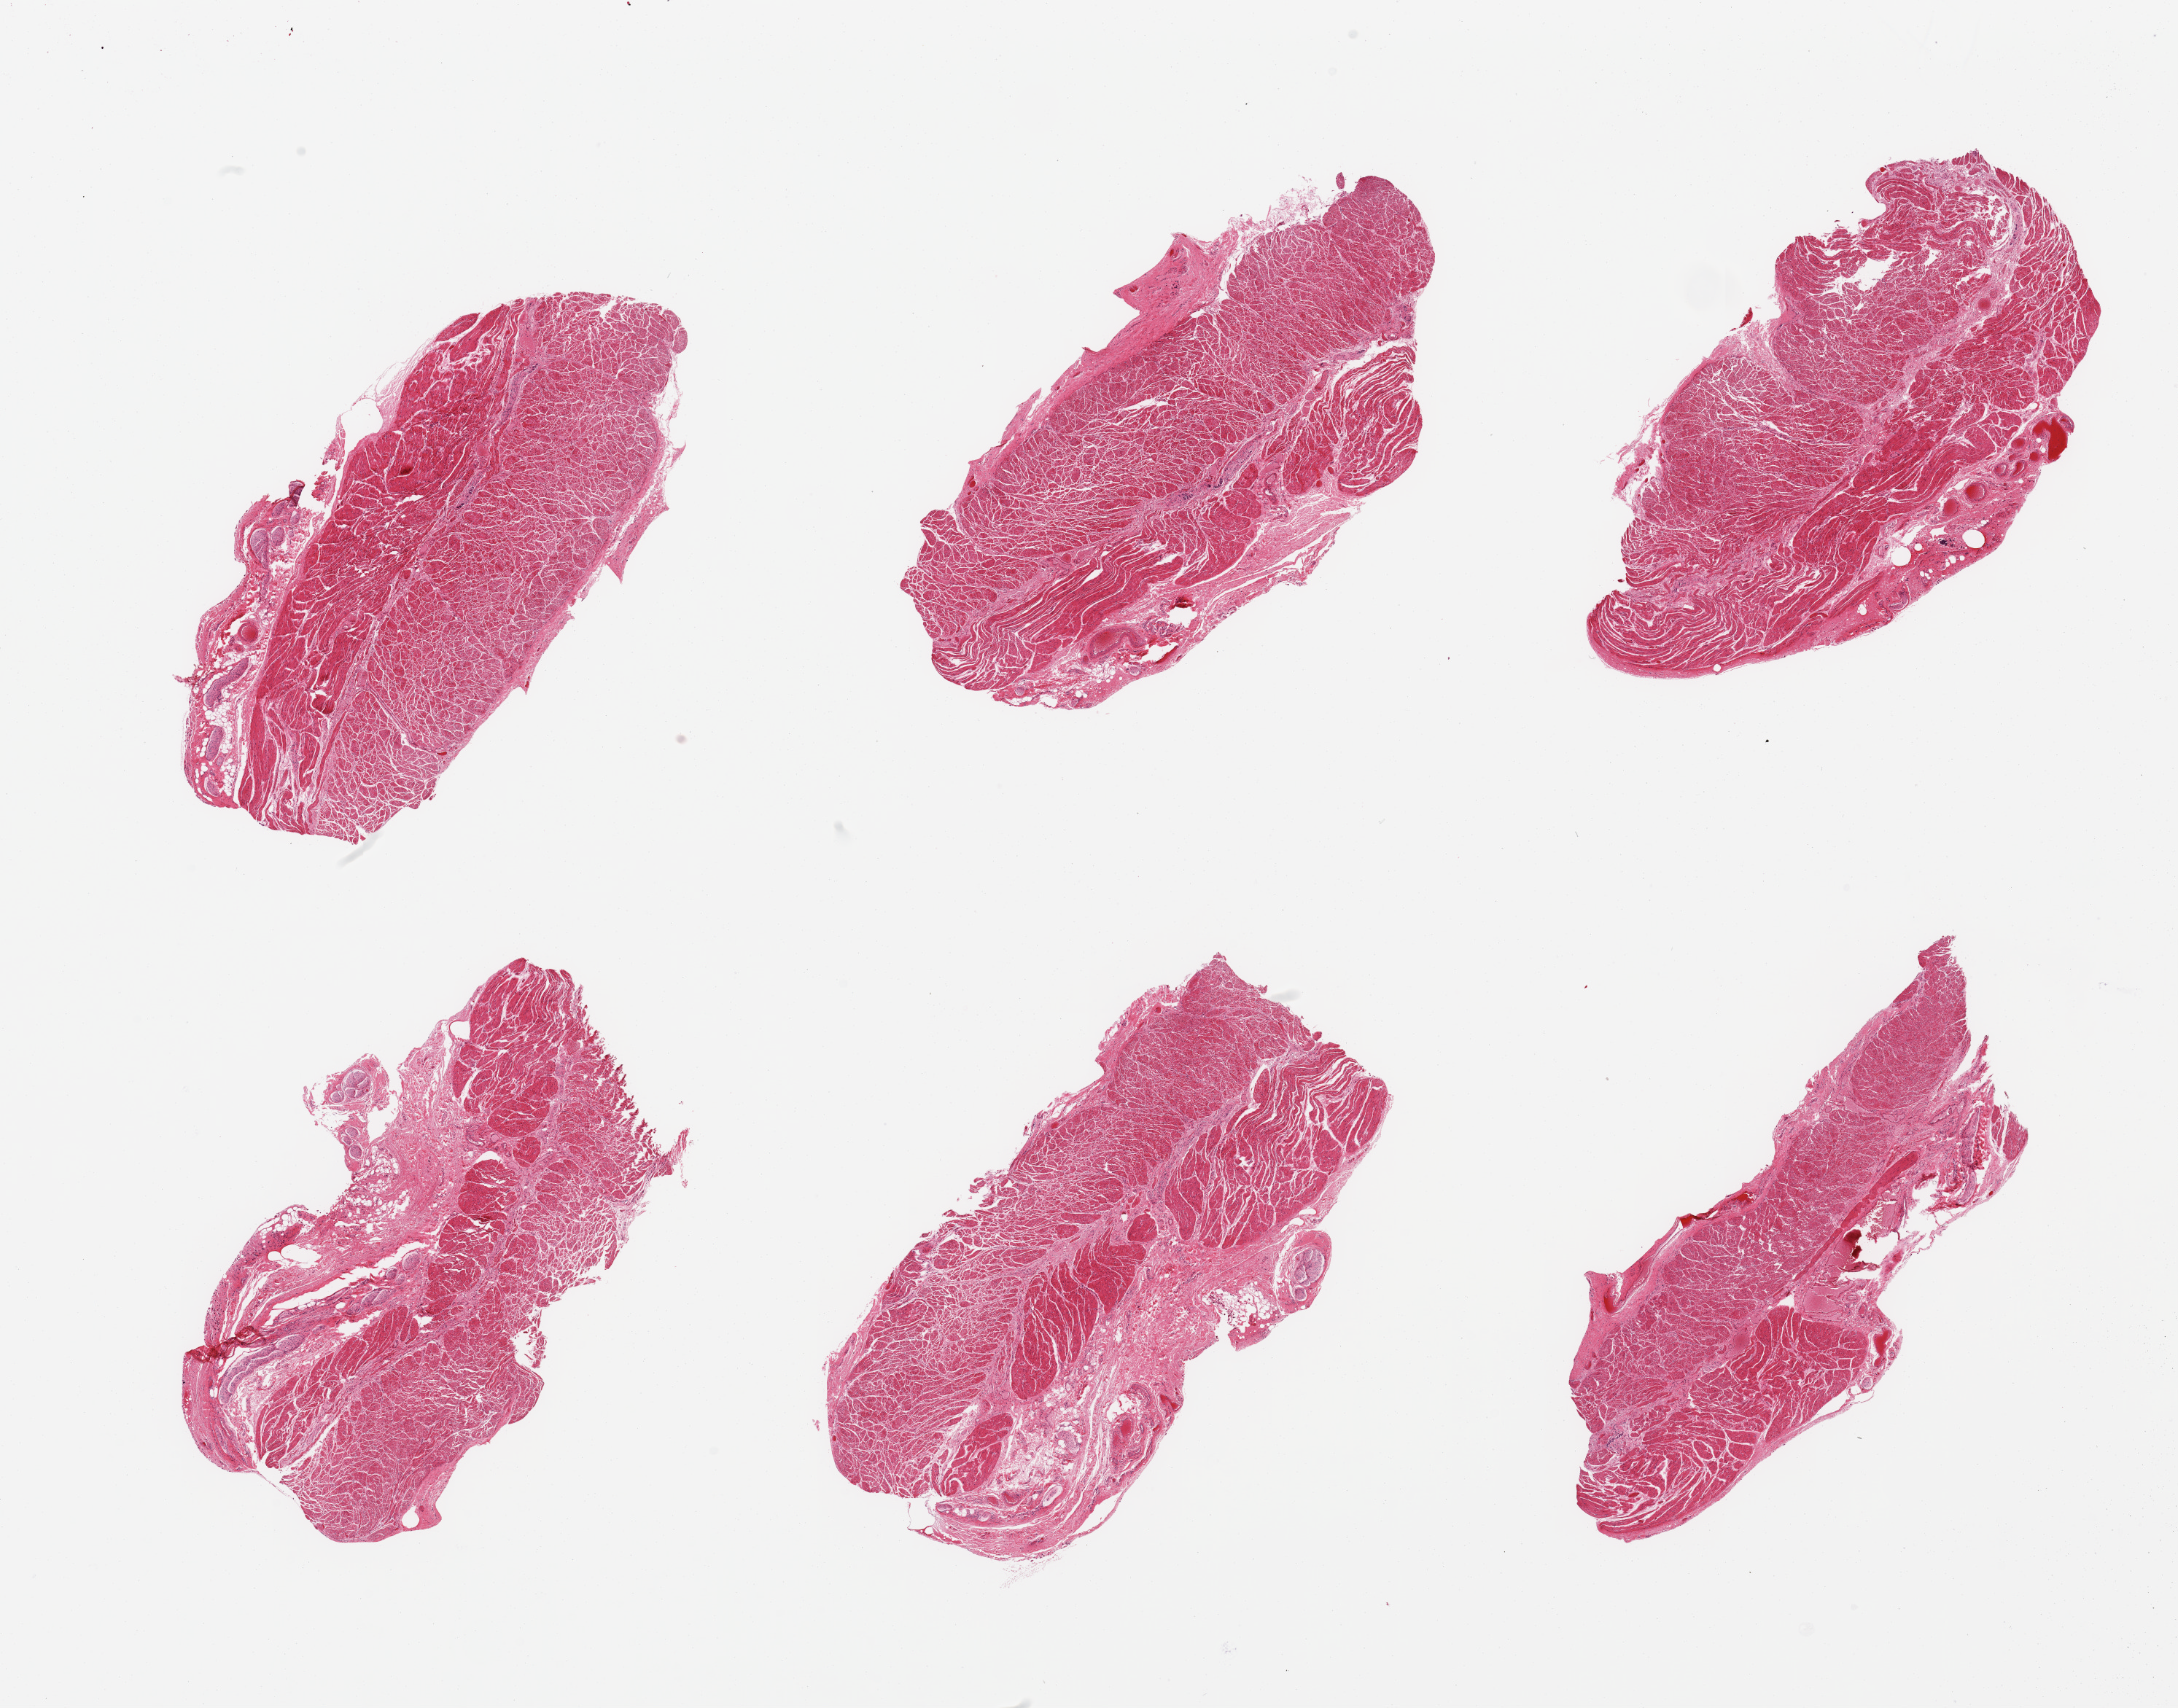
Digitized H&E-stained section, brightfield — a low-resolution overview of the entire scanned area, about 23.6 x 18.5 mm, PAXgene-fixed, paraffin-embedded tissue, section of esophageal muscle (target tissue), tissue donor sample. Donor sex: female.
Reviewer comment on this tissue sample: 6 pieces; 30% fibrous stroma on 2 pieces.